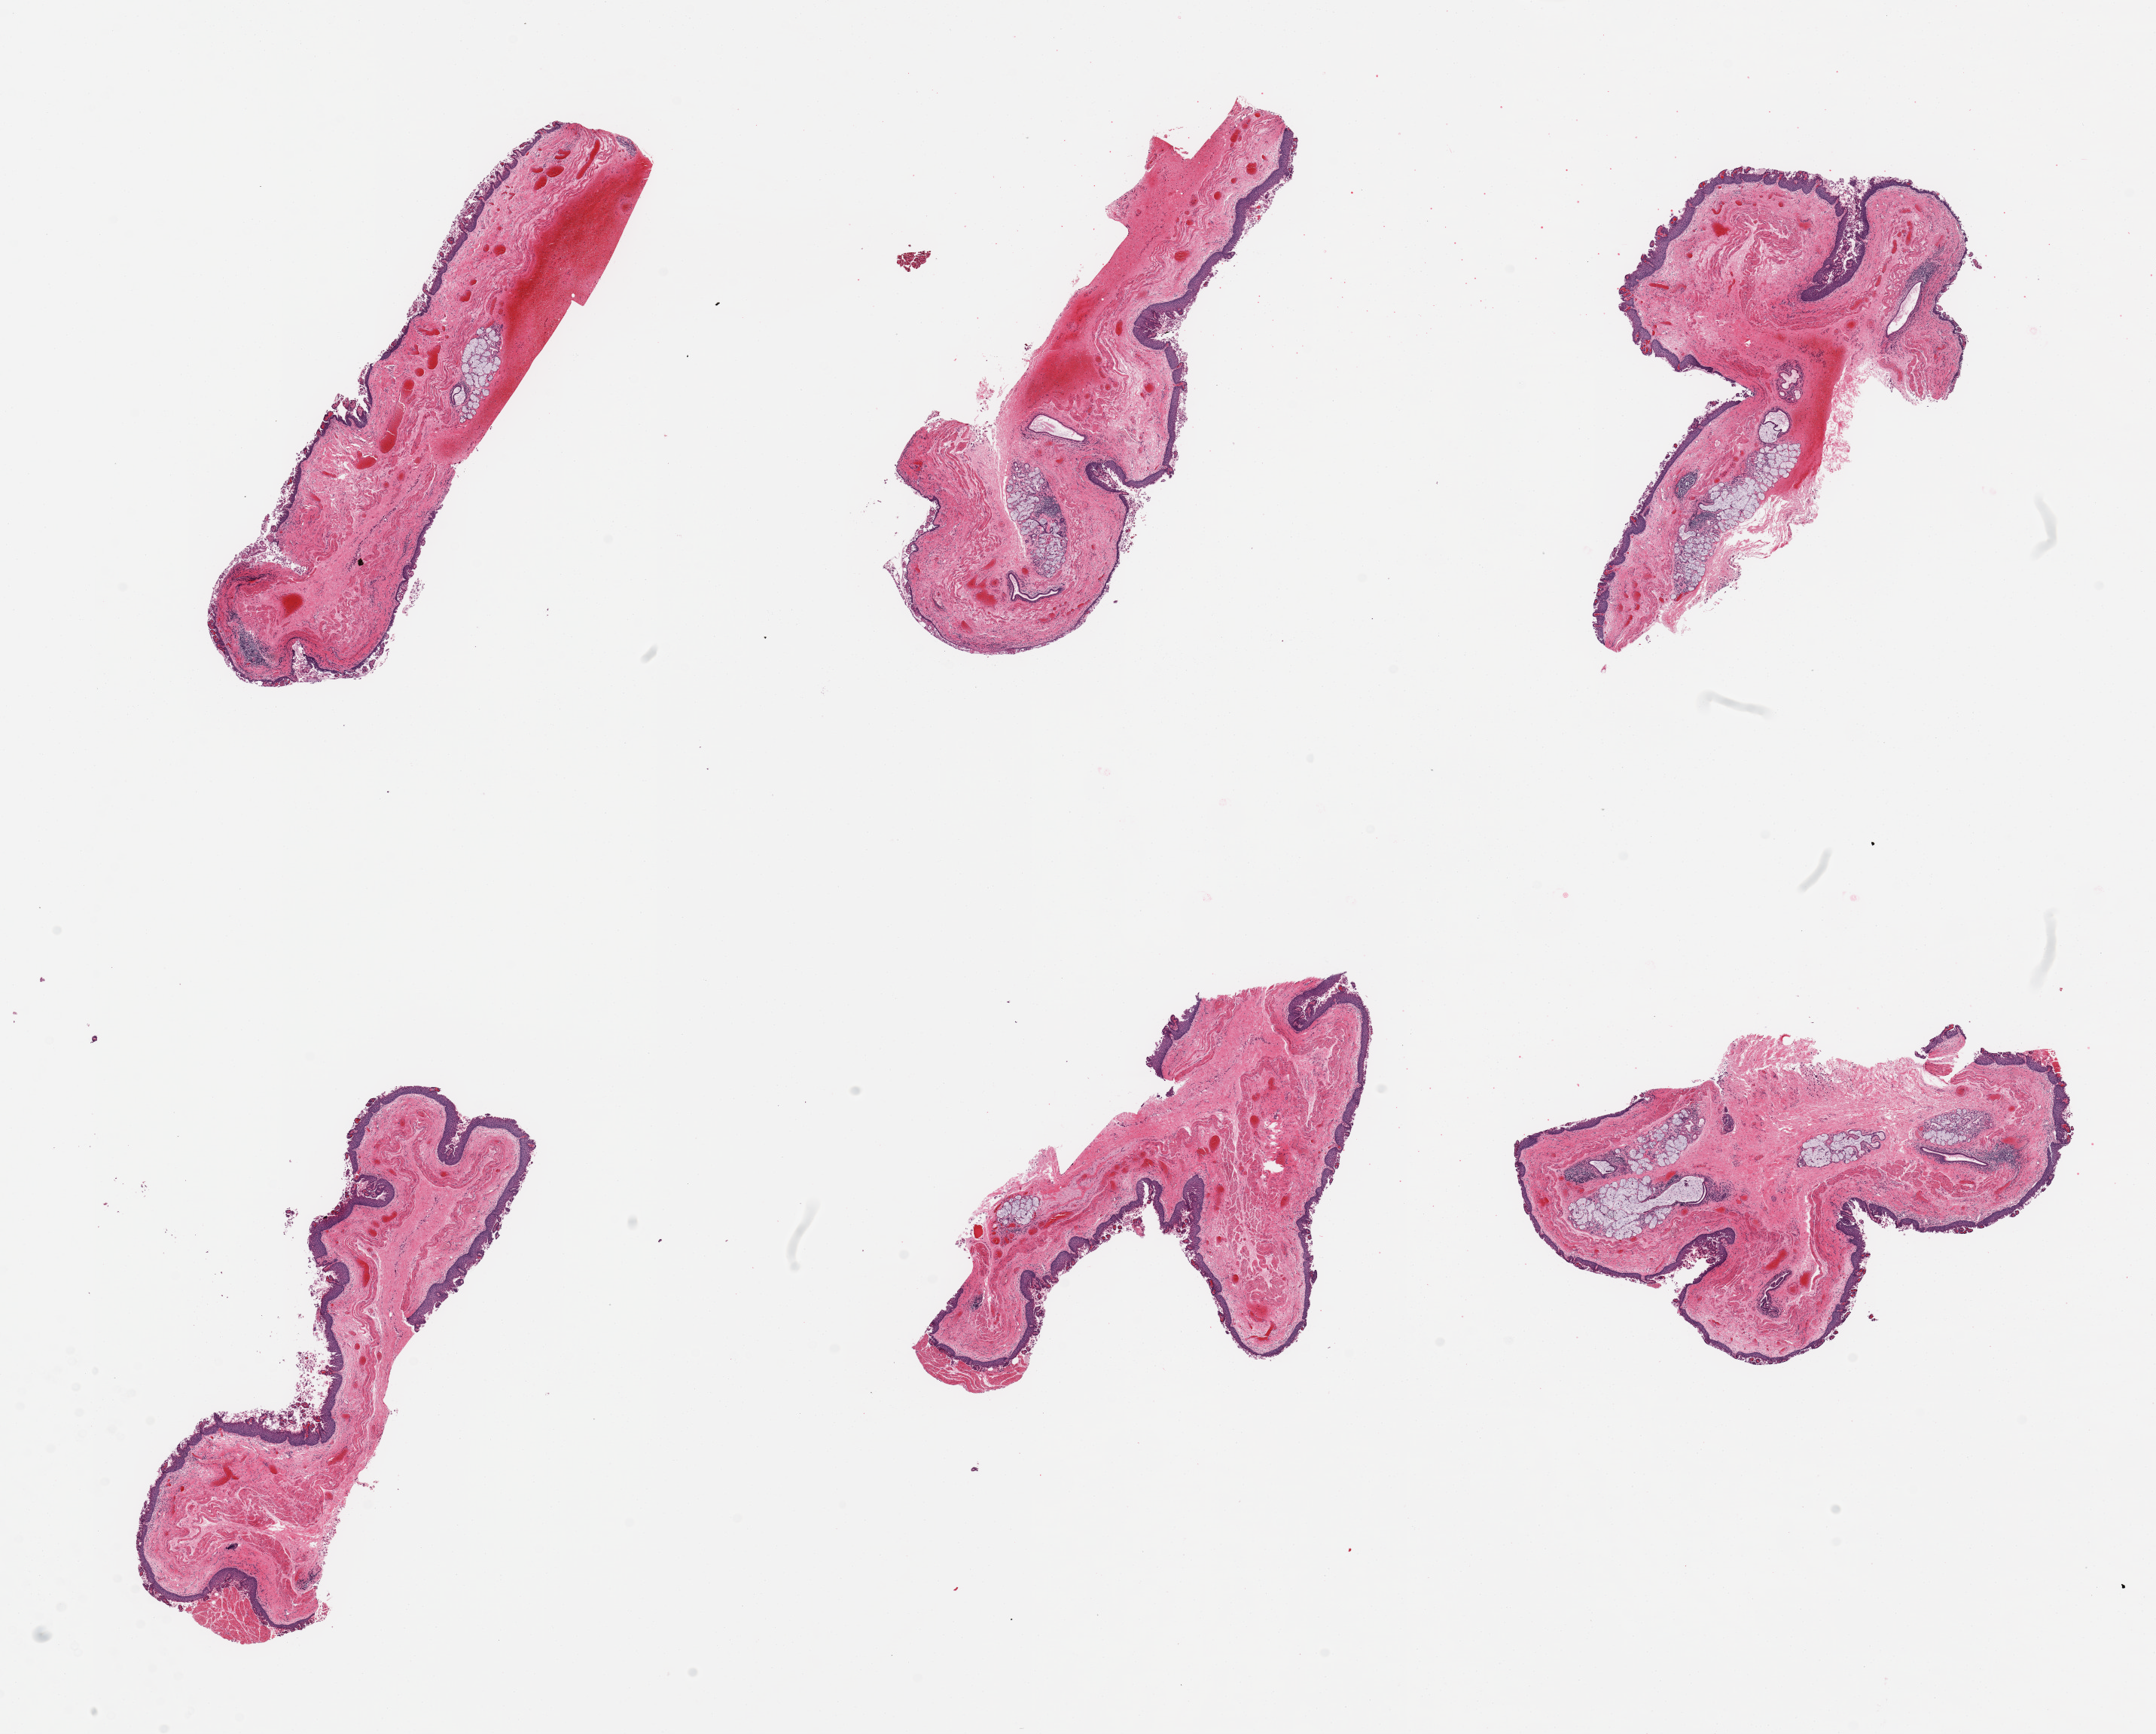
Haematoxylin and eosin whole-slide image, shown as a low-resolution overview of the whole scanned area (about 22.6 x 18.2 mm, acquisition: 20x scan), PAXgene-fixed, paraffin-embedded tissue, sampled site (target tissue): esophageal mucous membrane, donor tissue sample. Donor sex: male.
- pathologist's review note for this sample: 6 pieces, squamous mucosa up to ~0.2mm, partially sloughing; Submucosa mucus glands abundant